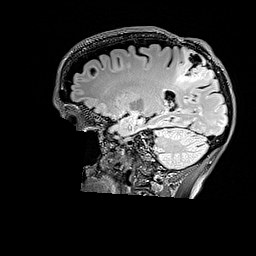
Brain MRI from a brain-tumour surgery series, one sagittal slice; position 111 of 176 along the scan axis; T2 FLAIR; 1 mm slice thickness; 256 × 256 image matrix, field of view 256 × 256 mm. From the clinical record (not read from this slice): histopathology: Astrocytoma; WHO grade: 3; IDH mutation: yes.
Annotated regions visible in this slice (outlined manually by an expert reader):
- tumour: box from (x=175, y=49) to (x=216, y=87) px
- tumour: (x=185, y=59)–(x=215, y=83)